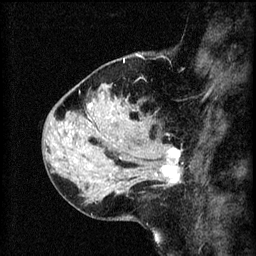
Breast MRI (dynamic contrast-enhanced), one sagittal slice. Position 22 of 60 along the scan axis. 3 images stored at this slice position (order not interpretable as contrast timing). 1.5 T. TE 4.2 ms, TR 8.2 ms. 2 mm slice thickness. 256 × 256 image matrix. Patient: female, 37 years.
Annotated regions visible in this slice (semi-automatic segmentation, software-assisted and operator-edited):
- analysis volume of interest (the breast-tissue region the enhancement analysis was run in; not a lesion): bounding box (x1, y1, x2, y2) in pixels: (124, 138, 183, 195)
- tumour enhancement mask (voxels above the 70 % enhancement threshold inside the analysis volume of interest): (161, 148, 182, 187)